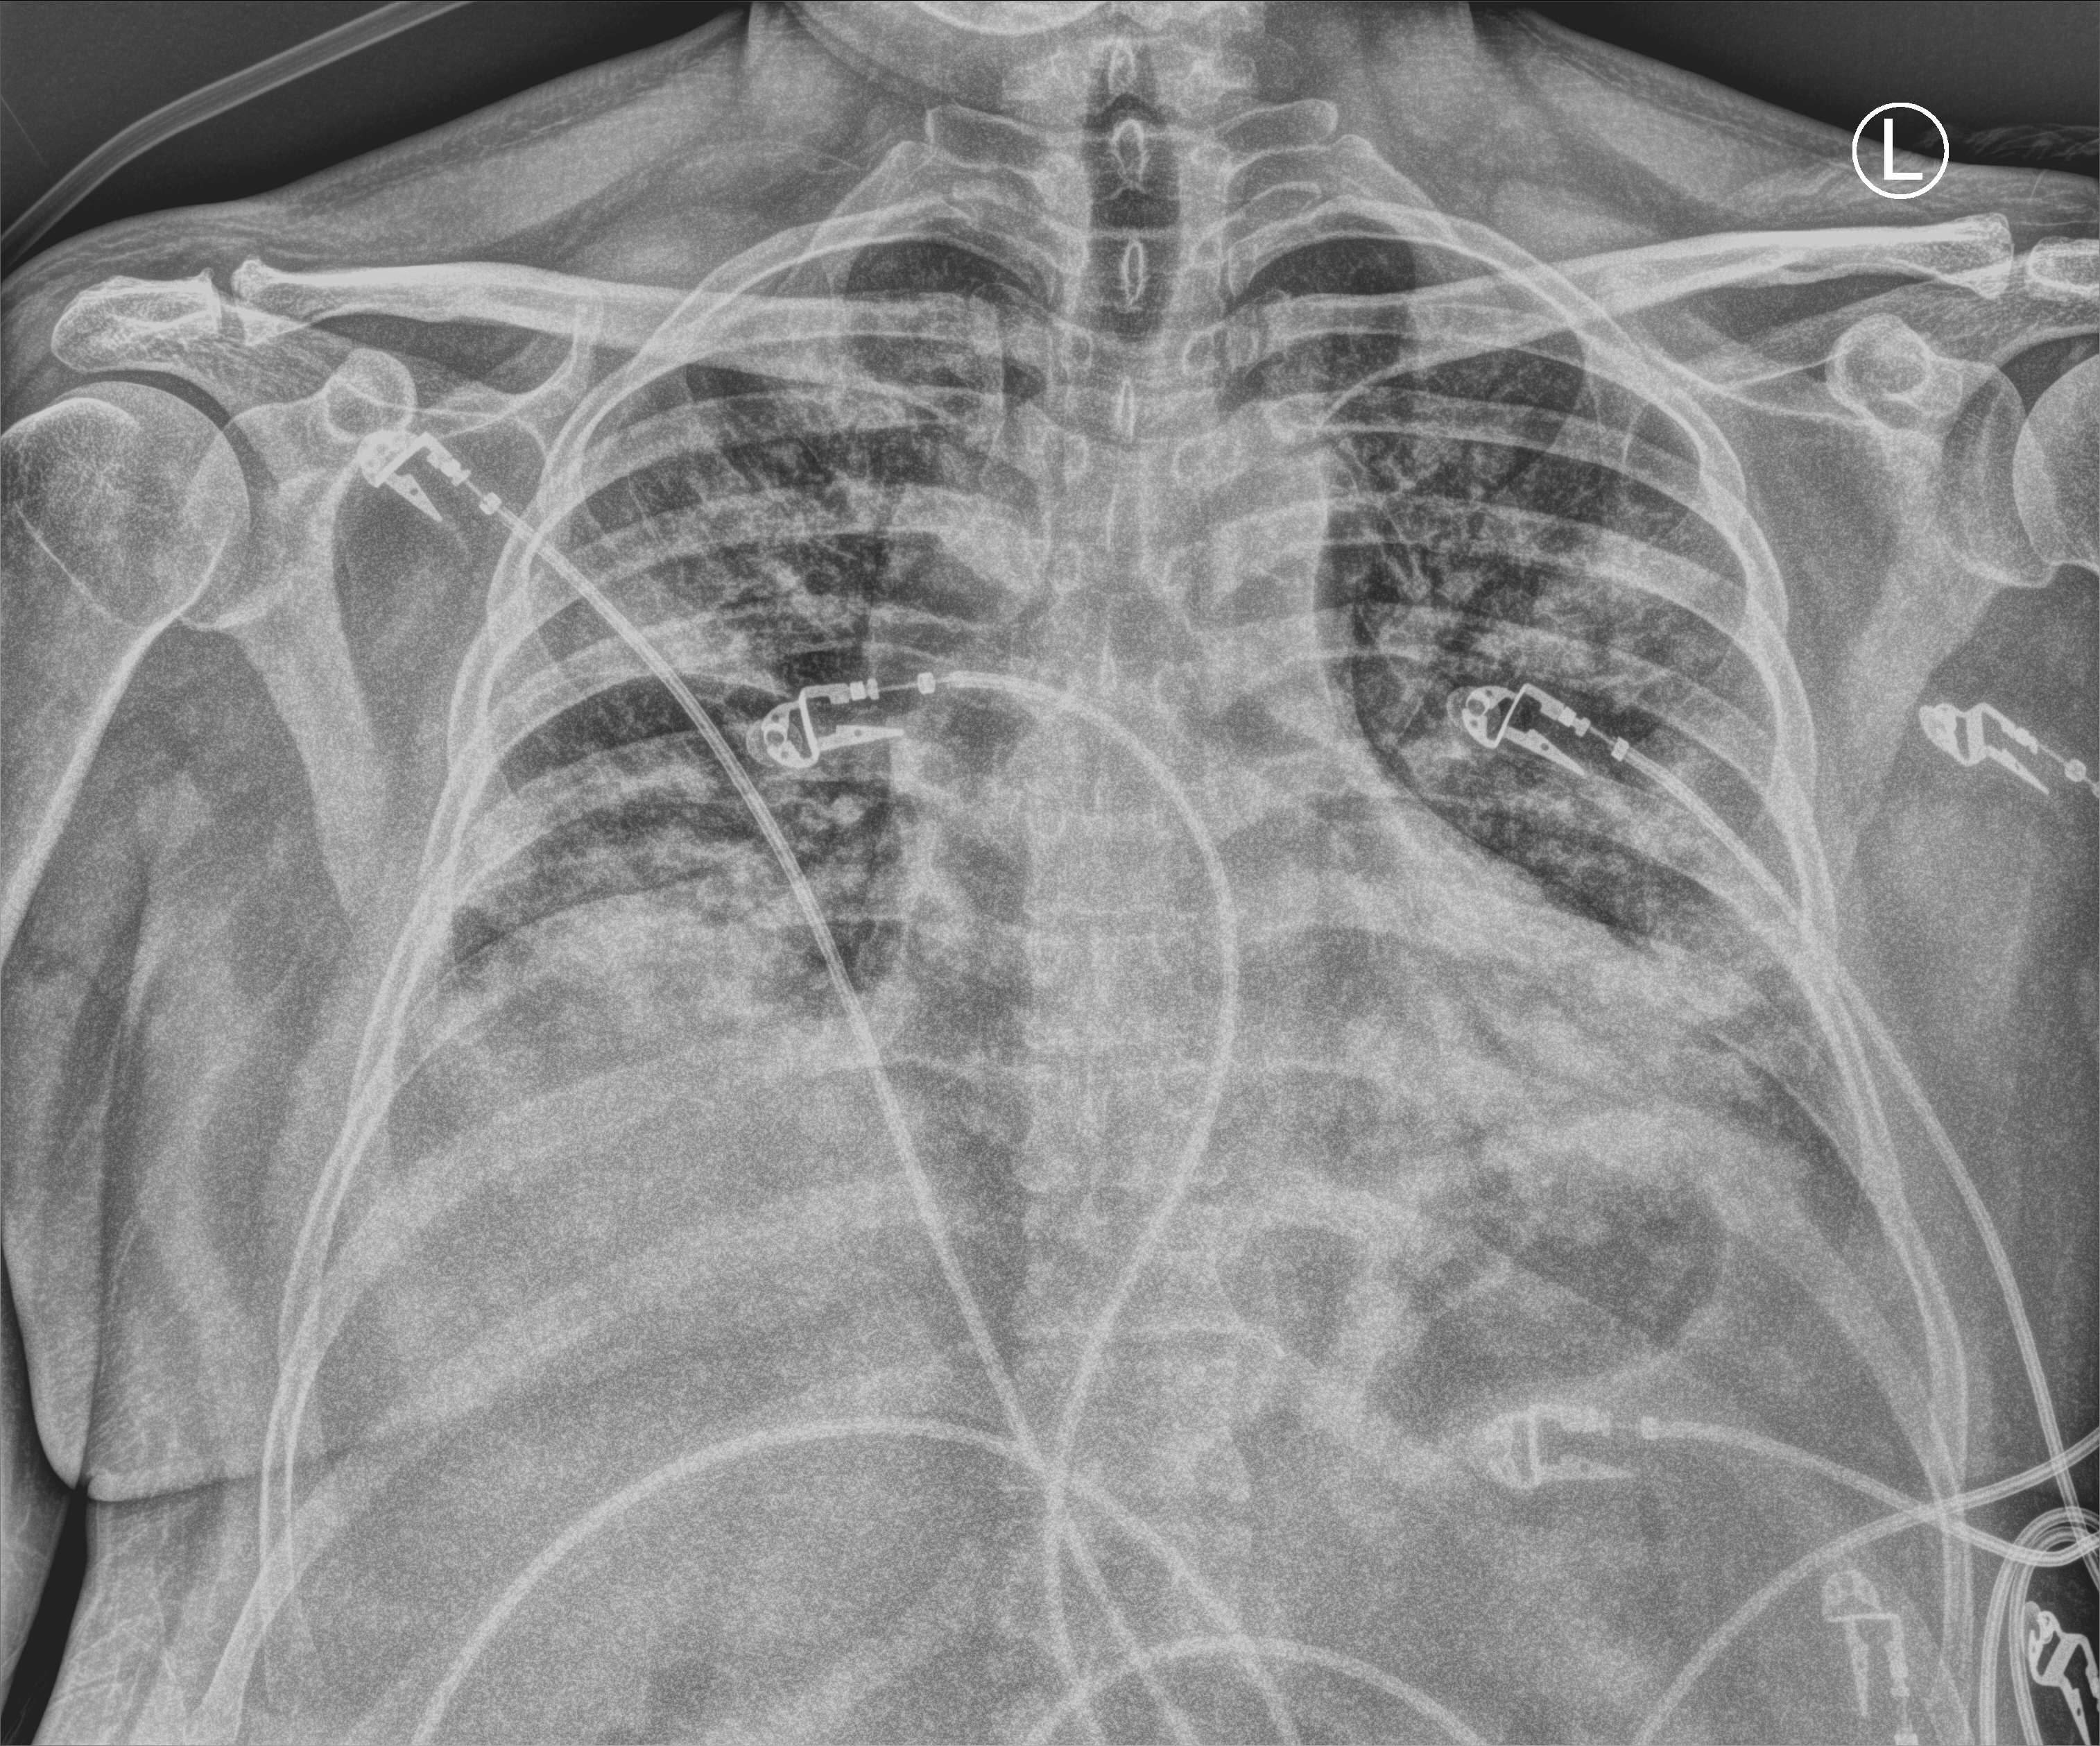
Chest X-ray (portable). Patient hospitalised with COVID-19; male, aged 18–59 years.
From the hospital-stay record, not from the radiograph (when in the stay this image was taken is not recorded): mechanically ventilated during this hospital stay: no.